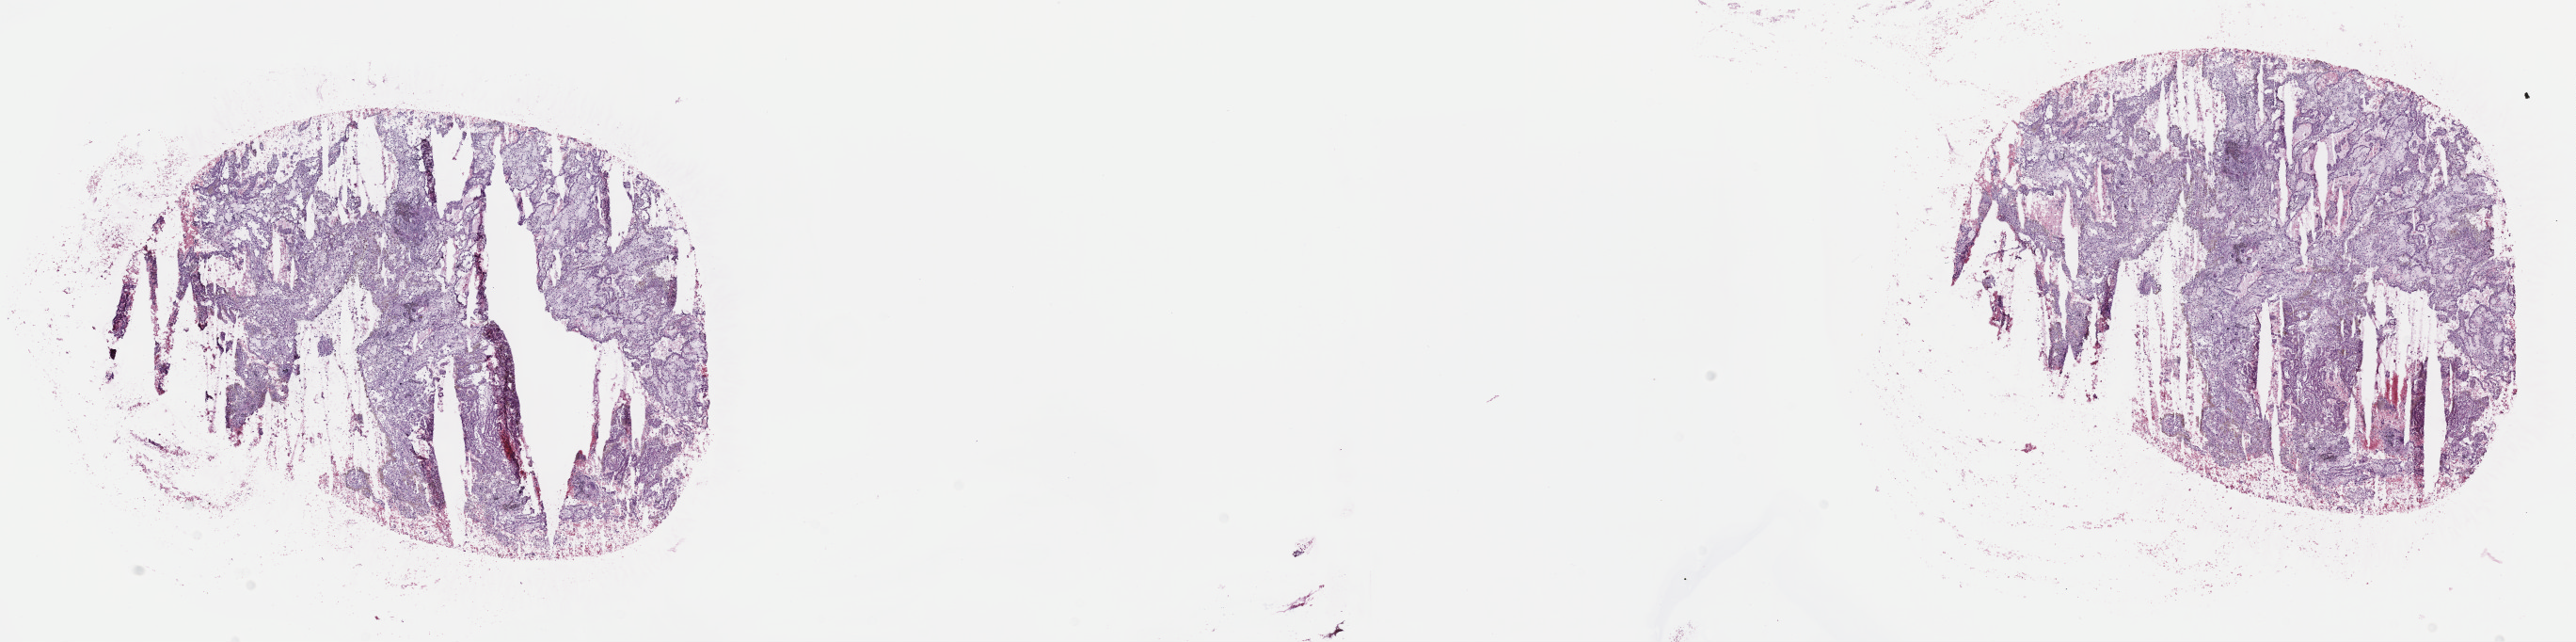
H&E whole-slide image — low-resolution overview of the scanned area, about 22.1 x 5.5 mm (acquisition: 40x scan); frozen section from the top of the tissue portion; primary tumour sample from the kidney. Male patient; age at initial diagnosis 69 years. Slide review estimates, as recorded: tumour cells 65%, tumour nuclei 70%, normal cells 0%, stromal cells 30%, necrosis 5%. Infiltration values recorded for this section: lymphocyte infiltration 5%, monocyte infiltration 10%, neutrophil infiltration 0%.
Diagnosis: Papillary adenocarcinoma, NOS. AJCC pathologic stage: I (7th edition).